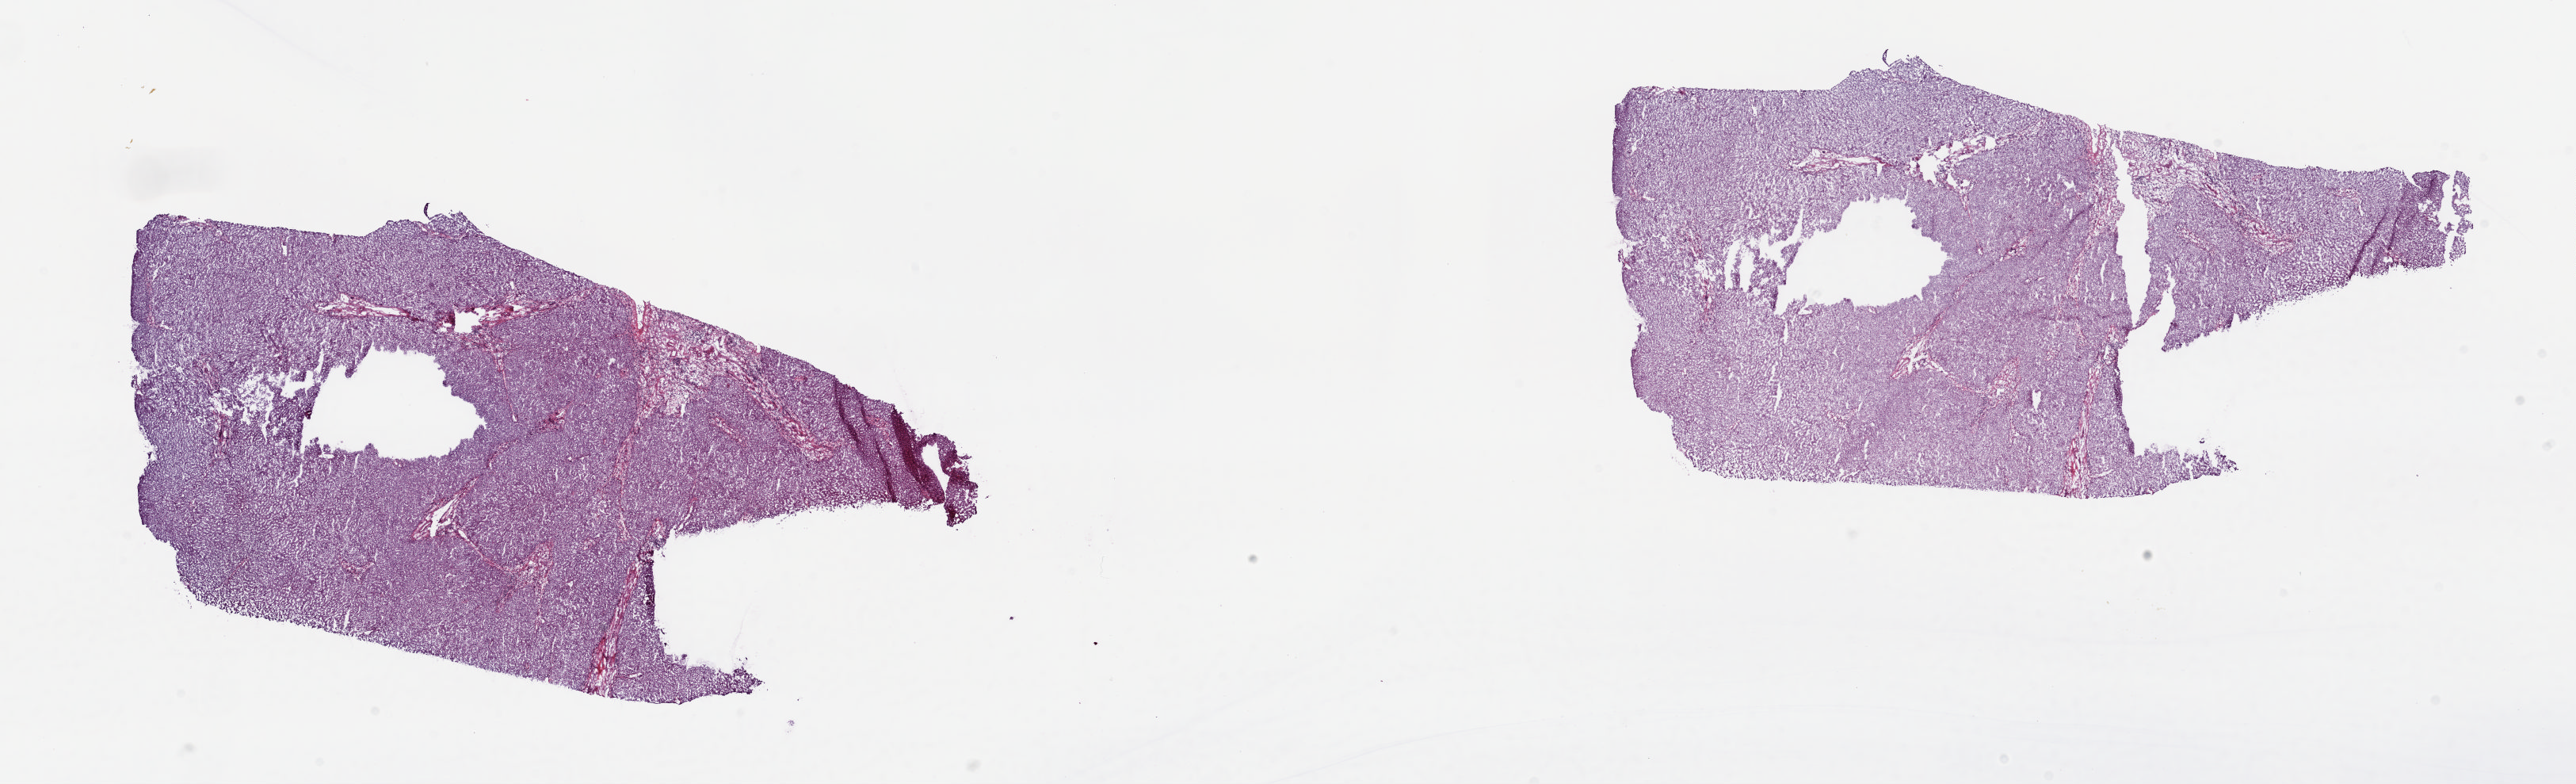
Whole-slide histology image, Hematoxylin and eosin (H&E) stained — low-resolution overview of the scanned area, about 25.8 x 7.8 mm (slide scanned at 20x). Frozen section from the top of the tissue portion. Solid tissue normal (non-tumour tissue) sample from the bile duct. Female patient; age at initial diagnosis 77 years. Slide review estimates, as recorded: tumour cells 0%, tumour nuclei 0%, normal cells 100%, stromal cells 0%, necrosis 0%. Inflammatory infiltration, as recorded: lymphocyte infiltration 0%, monocyte infiltration 0%, neutrophil infiltration 0%.
This section: solid tissue normal (non-tumour) sample from the same patient. Patient diagnosis: Cholangiocarcinoma (intrahepatic bile duct).